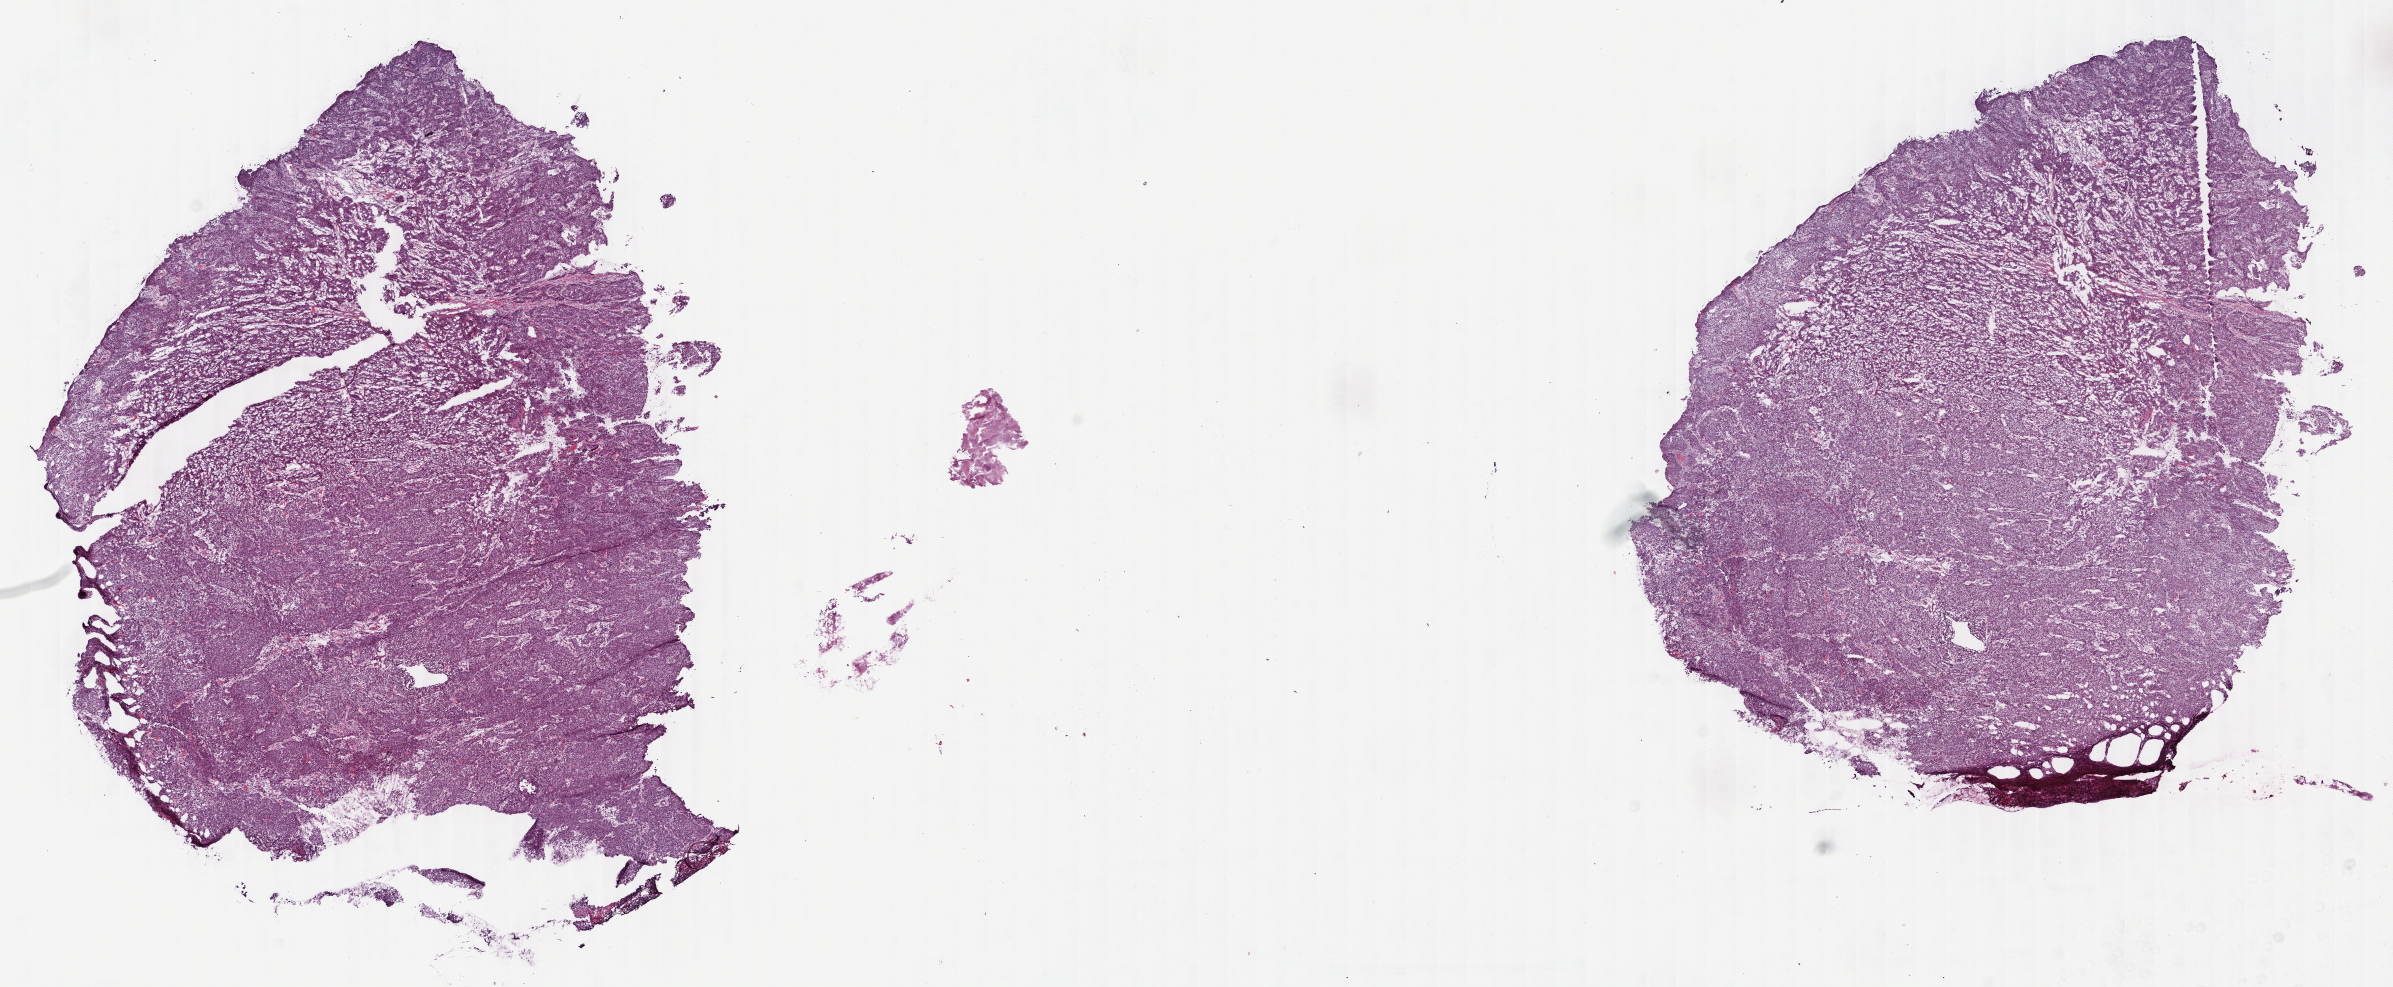
Hematoxylin and eosin (H&E) stained whole-slide image — a low-resolution overview of the entire scanned area, about 19.0 x 7.9 mm (acquisition: 40x scan), frozen section, primary tumour sample from the colon. Female patient; age at initial diagnosis 48 years. Composition of this section per pathologist review: tumour cells 95%, tumour nuclei 95%, normal cells 0%, stromal cells 4%, necrosis 1%. Inflammatory infiltration, as recorded: lymphocyte infiltration 1%, monocyte infiltration 1%, neutrophil infiltration 1%.
AJCC pathologic stage: II (5th edition). Diagnosis: Adenocarcinoma, NOS (ascending colon). Lymph nodes positive (case pathology): 0 of 16 examined. TNM: T3 N0 M0.